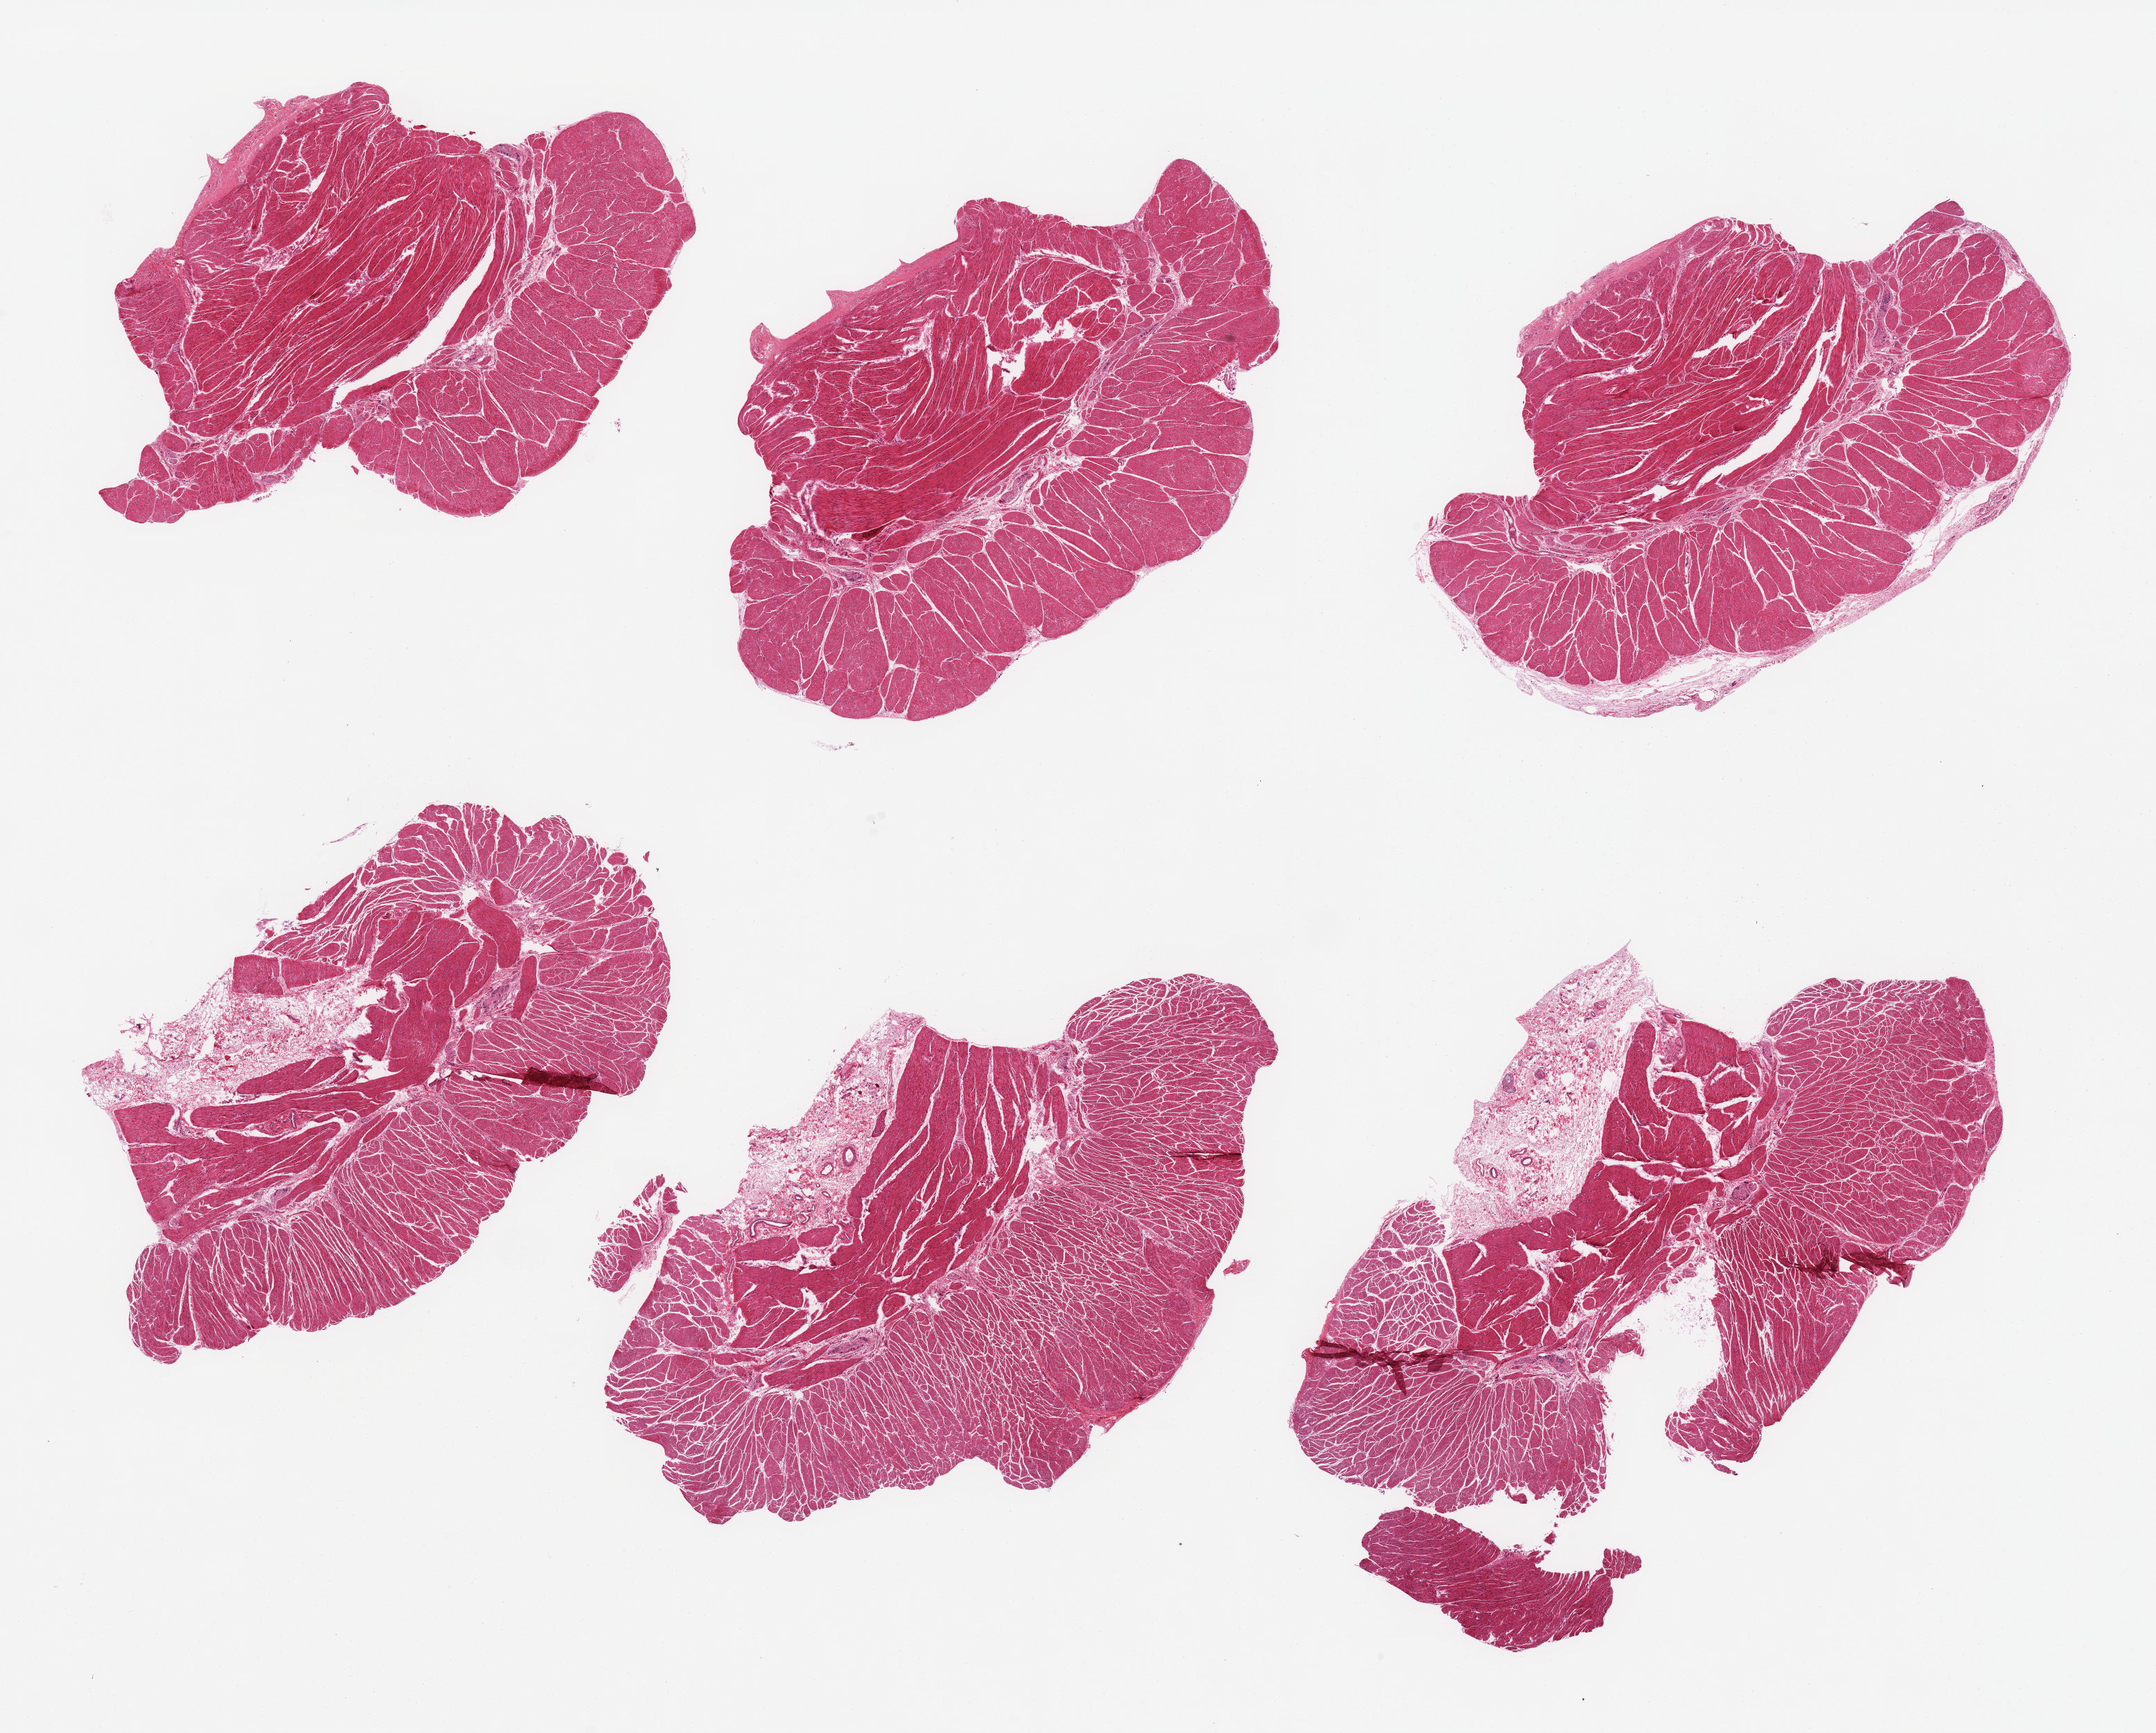
Hematoxylin and eosin (H&E) whole-slide image — low-resolution overview of the scanned area, about 24.6 x 19.8 mm. PAXgene-fixed, paraffin-embedded tissue. Target tissue: esophageal muscle. Tissue donor sample. Female donor.
• review note (as recorded): 6 pieces, confirmed target muscularis; few ~1.5mm nubbins of adherent serosa